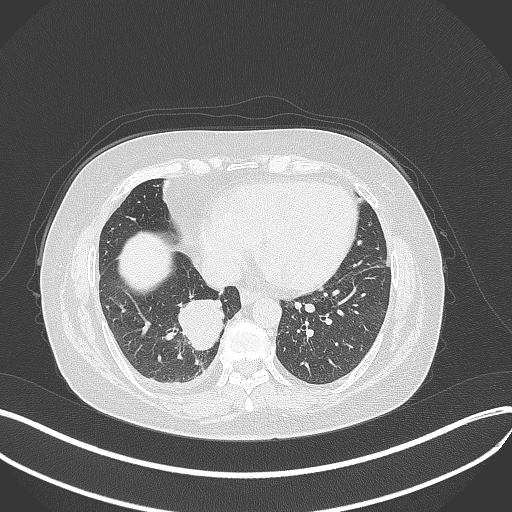
Chest CT, one axial slice; slice 122 of 381 in the series (ordered by position); reconstruction kernel B70f; 120 kVp; lung window (W 1500 / L -600 HU); 1 mm slice thickness; 512 × 512 image matrix, field of view 400 × 400 mm. Female patient, age 56 years. From the clinical record (not read from this slice): clinical TNM (as recorded): T2b N1 M0.
Structures marked on this image (rectangle marked by the reading radiologist):
- lung tumour (recorded histology: small cell carcinoma): bounding box [x1, y1, x2, y2] px = [174, 296, 227, 357]